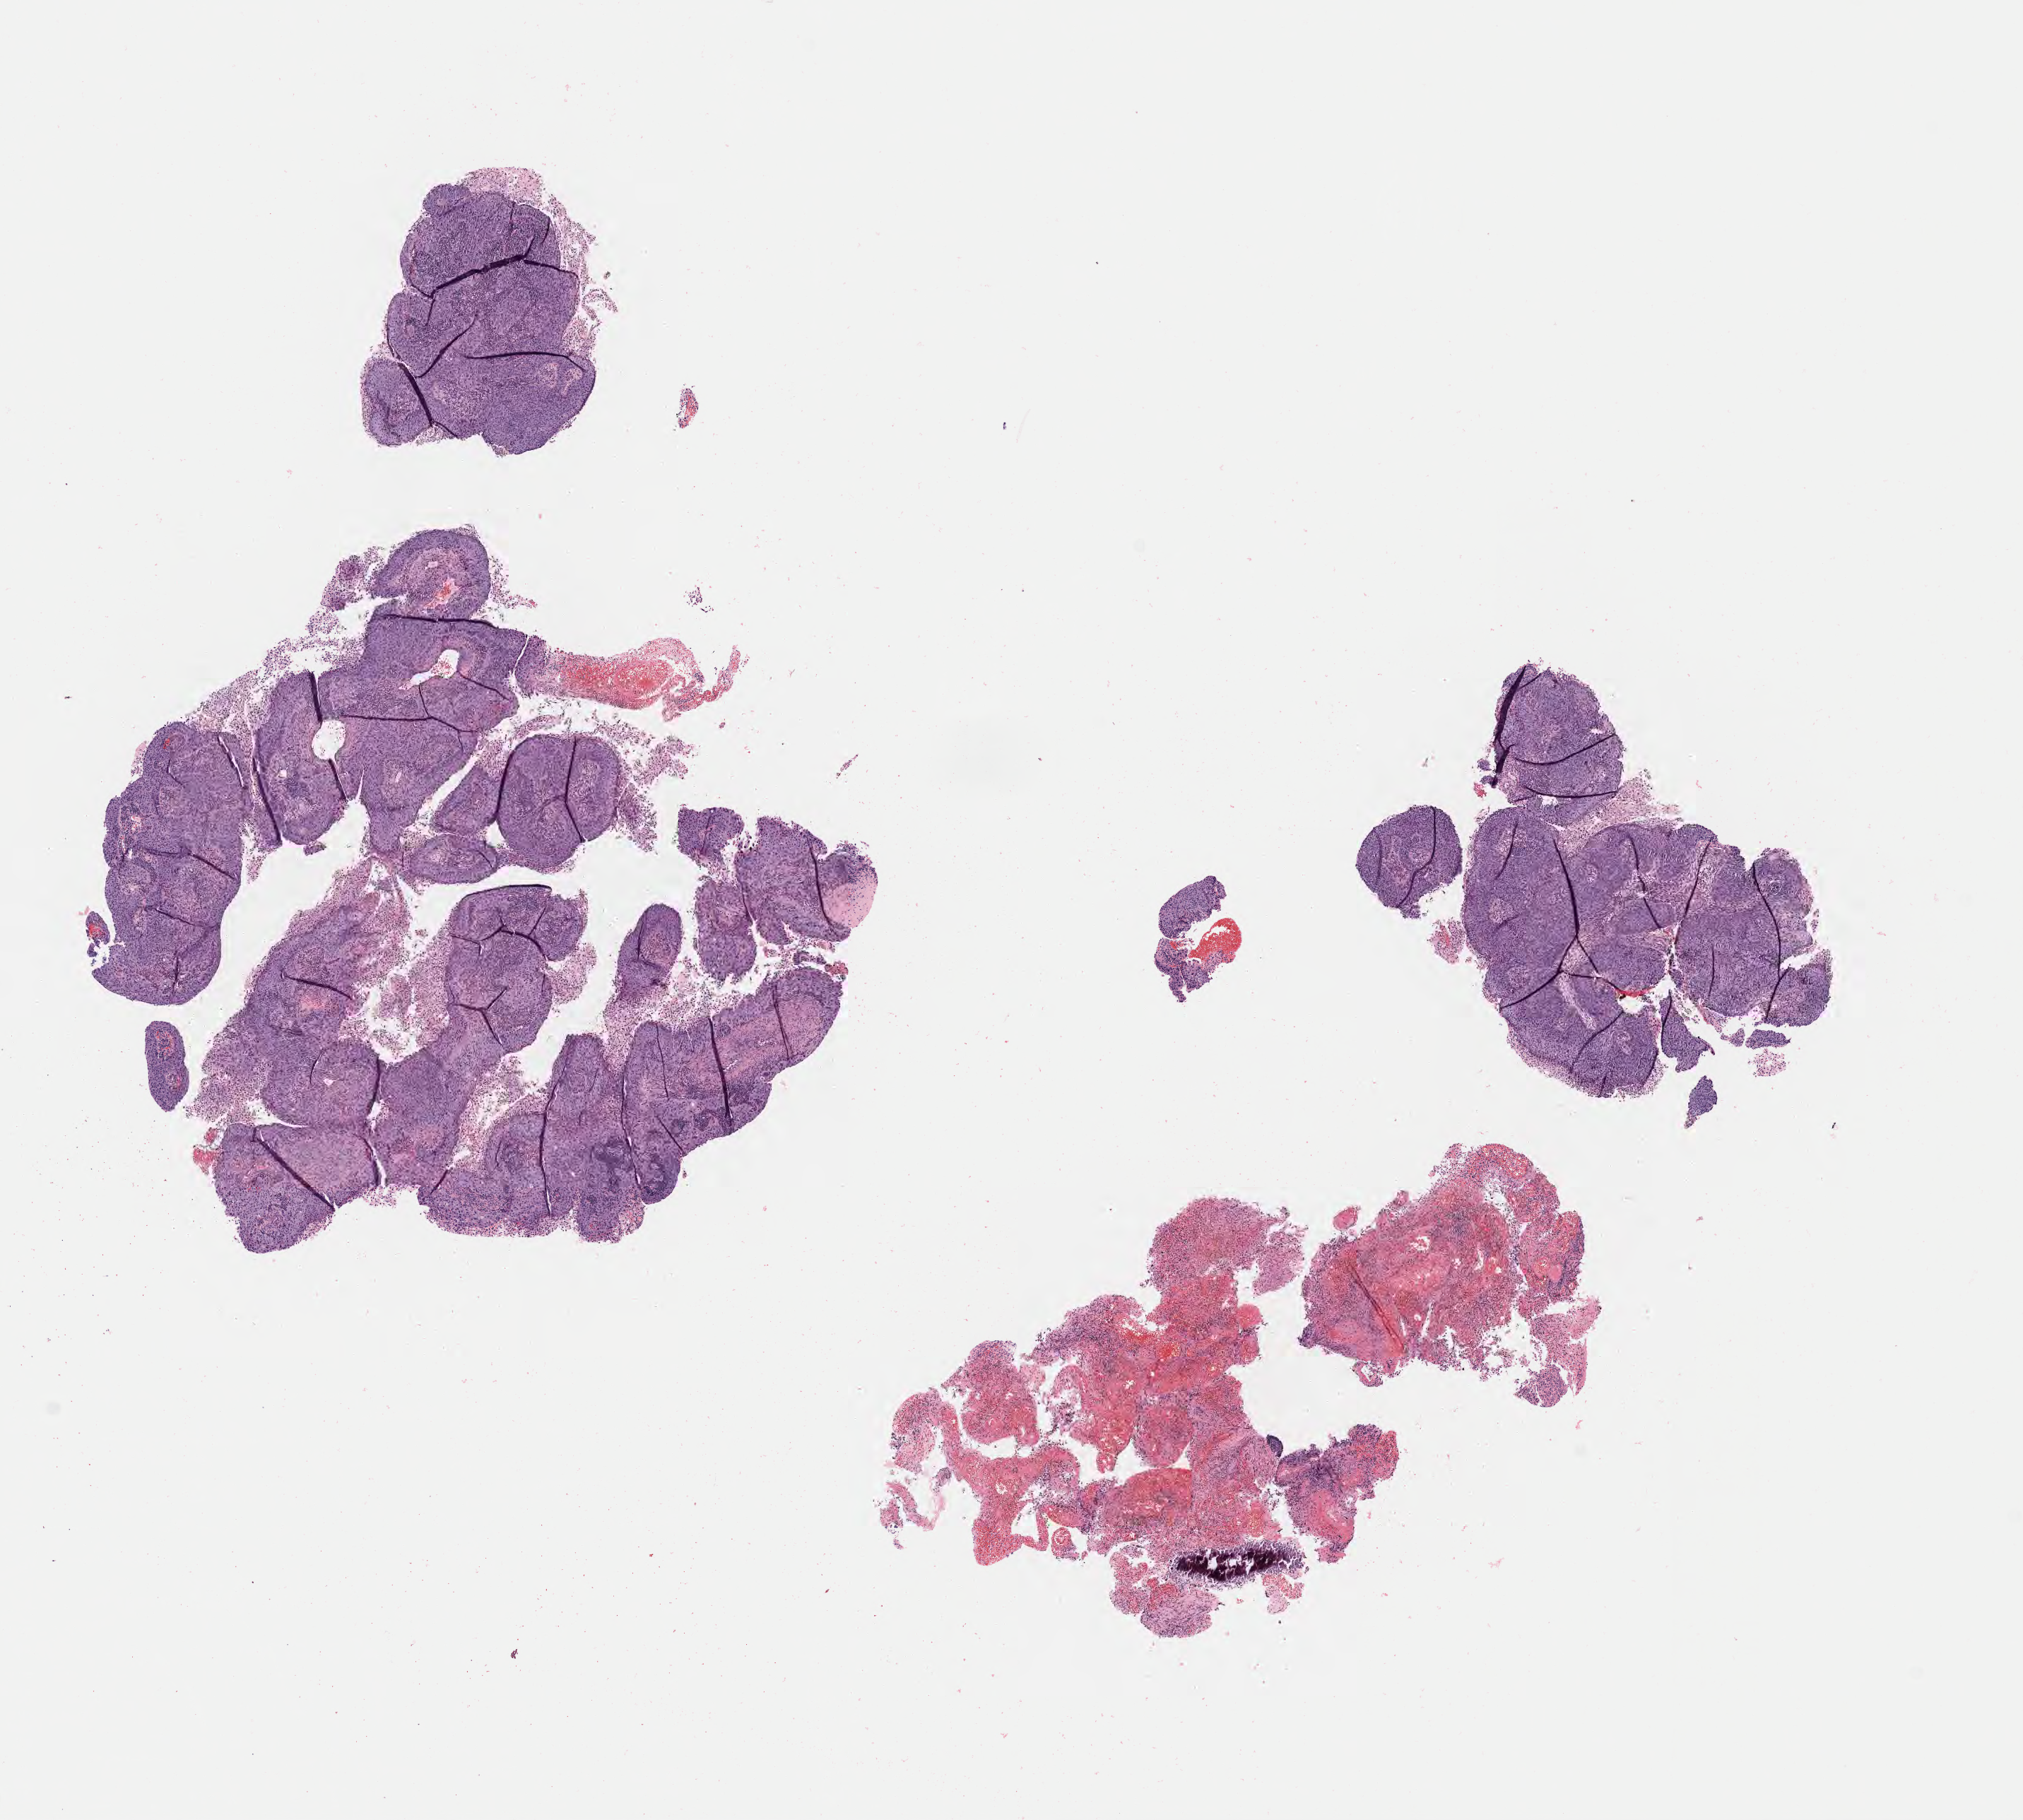
Whole-slide image, H&E stain, low-resolution overview of the scanned area, about 11.6 x 10.4 mm; specimen: tumor tissue; site: cervix. Patient female; age 59 years.
Diagnosis: Squamous cell carcinoma, large cell, nonkeratinizing, NOS.